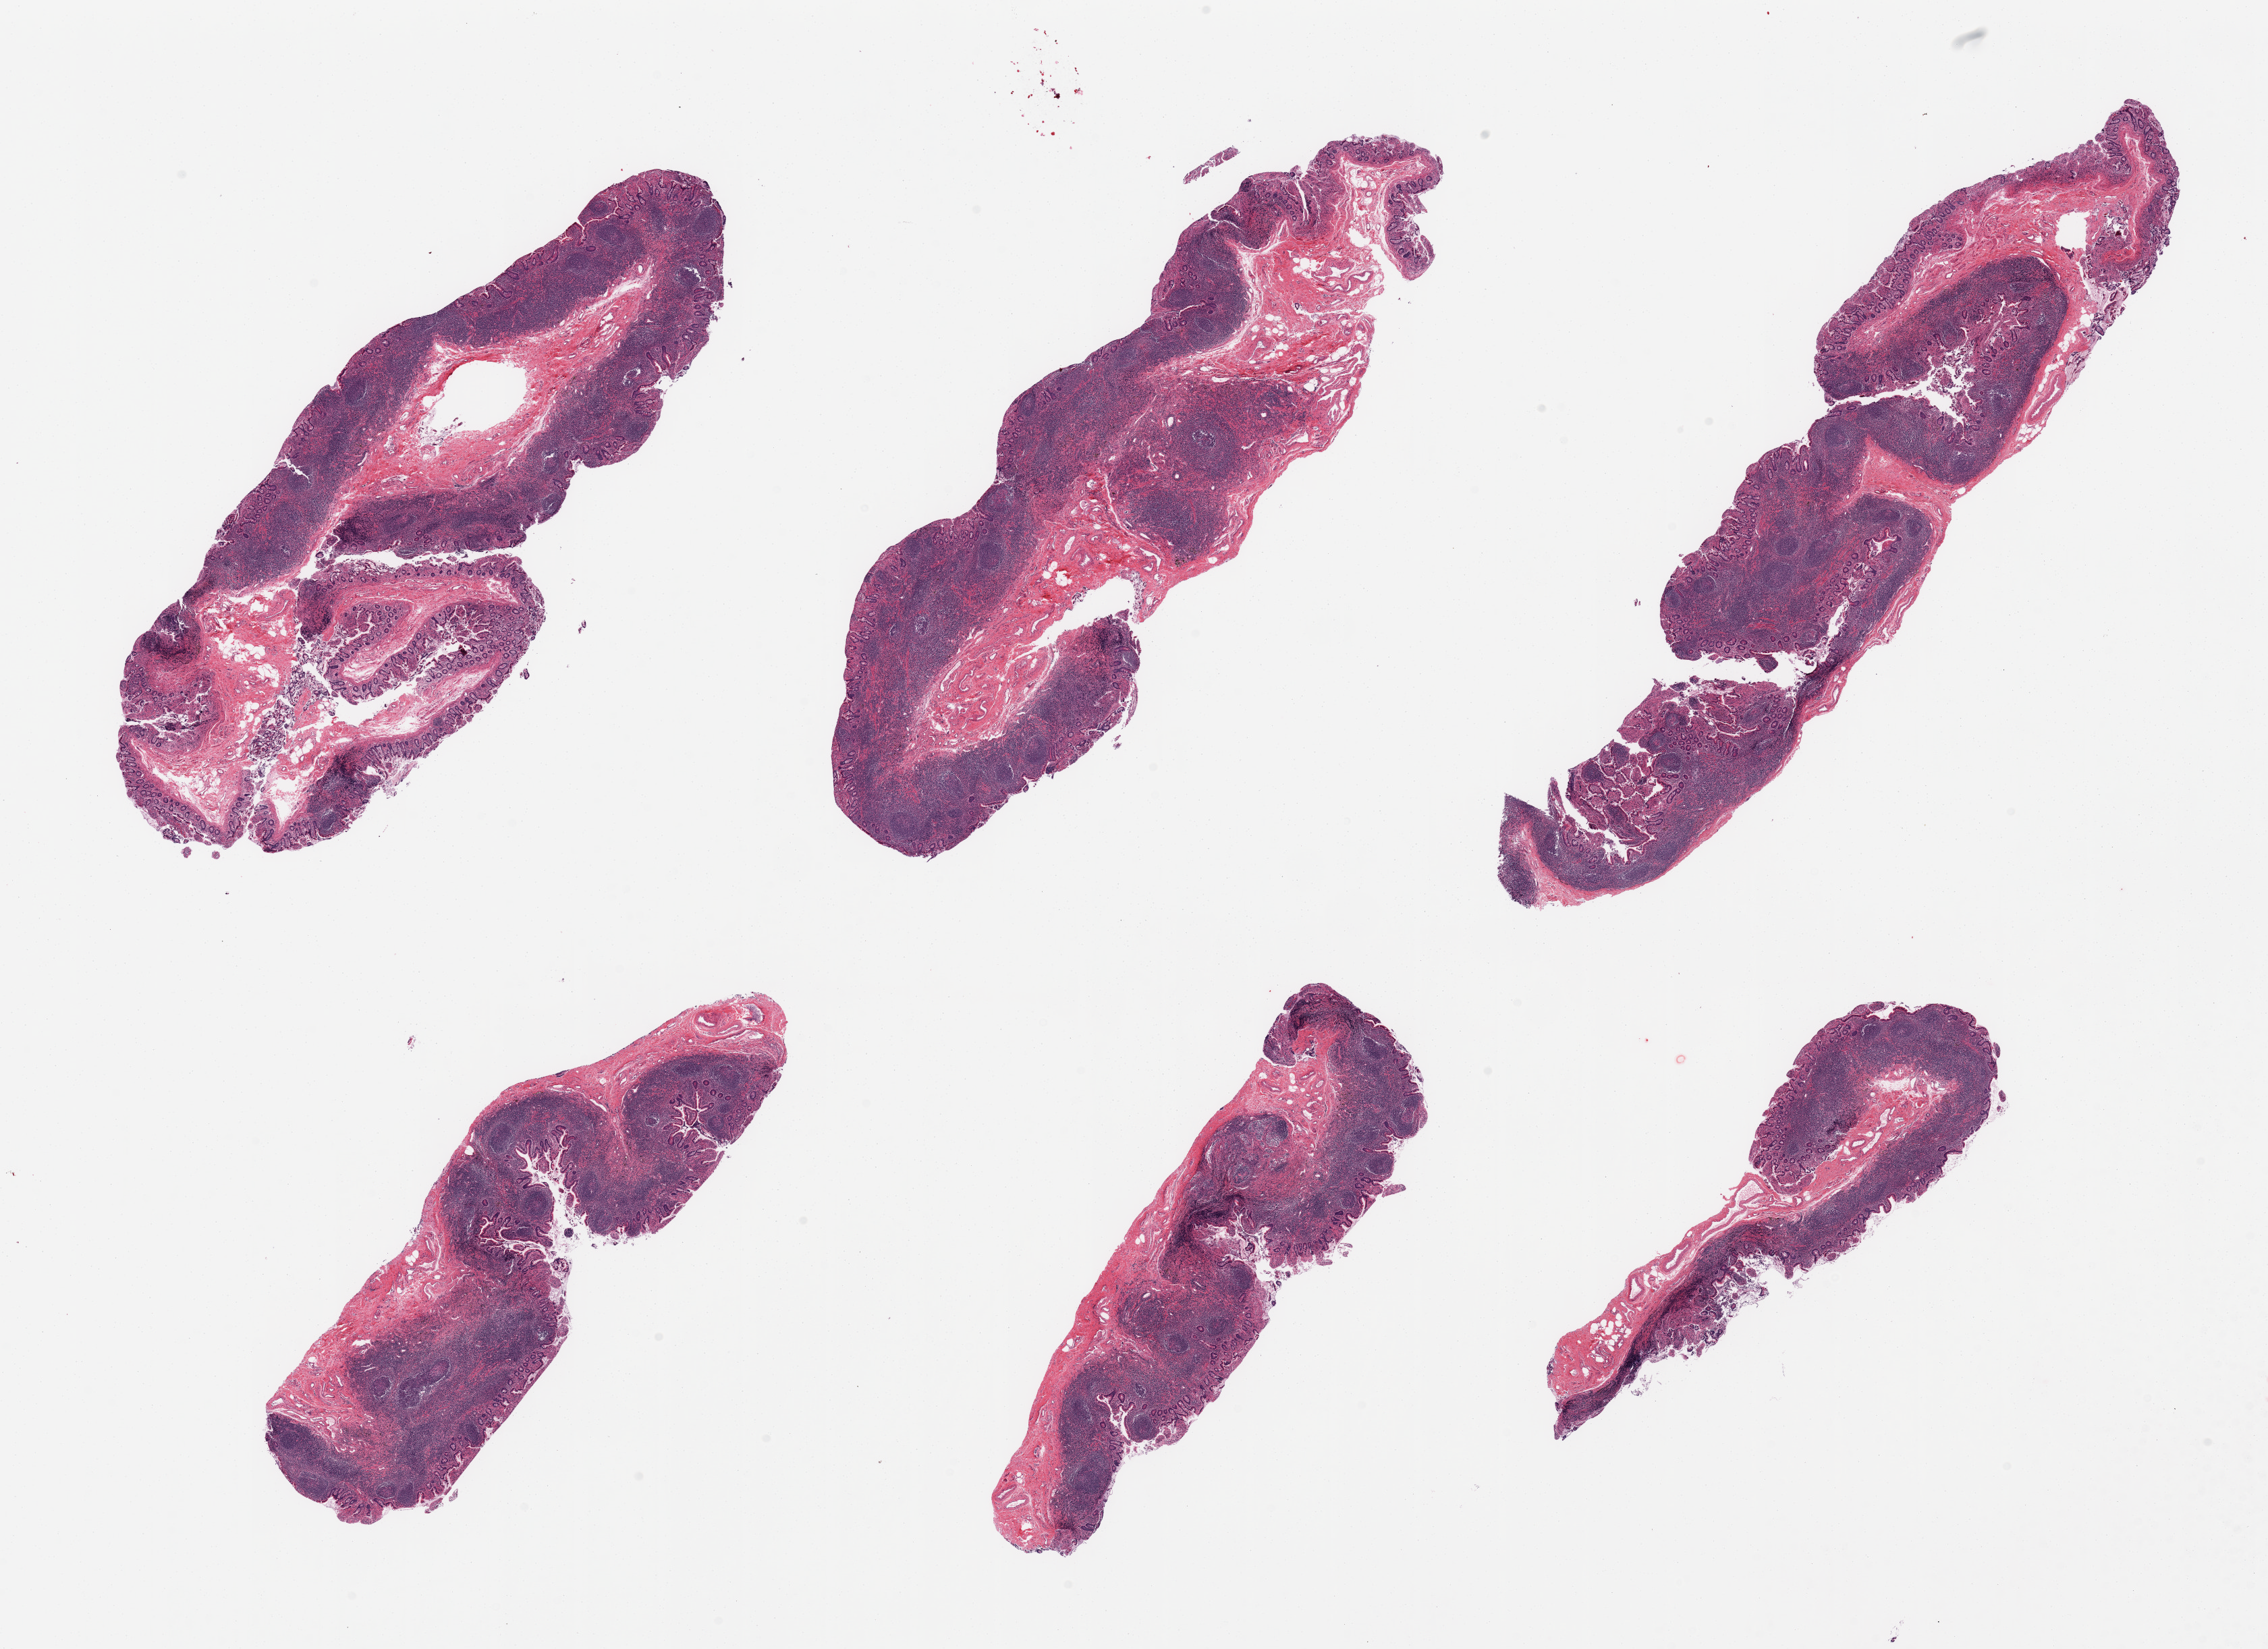
H&E whole-slide image, brightfield — whole scanned area (about 26.6 x 19.3 mm, acquisition: 20x scan) shown as a low-resolution overview. PAXgene-fixed paraffin-embedded (PFPE) section. Target tissue: ileum. Tissue donor sample.
Review note (as recorded): 6 pieces, unusually abundant and well preserved lymphoid aggregates are ~50% total specimen.